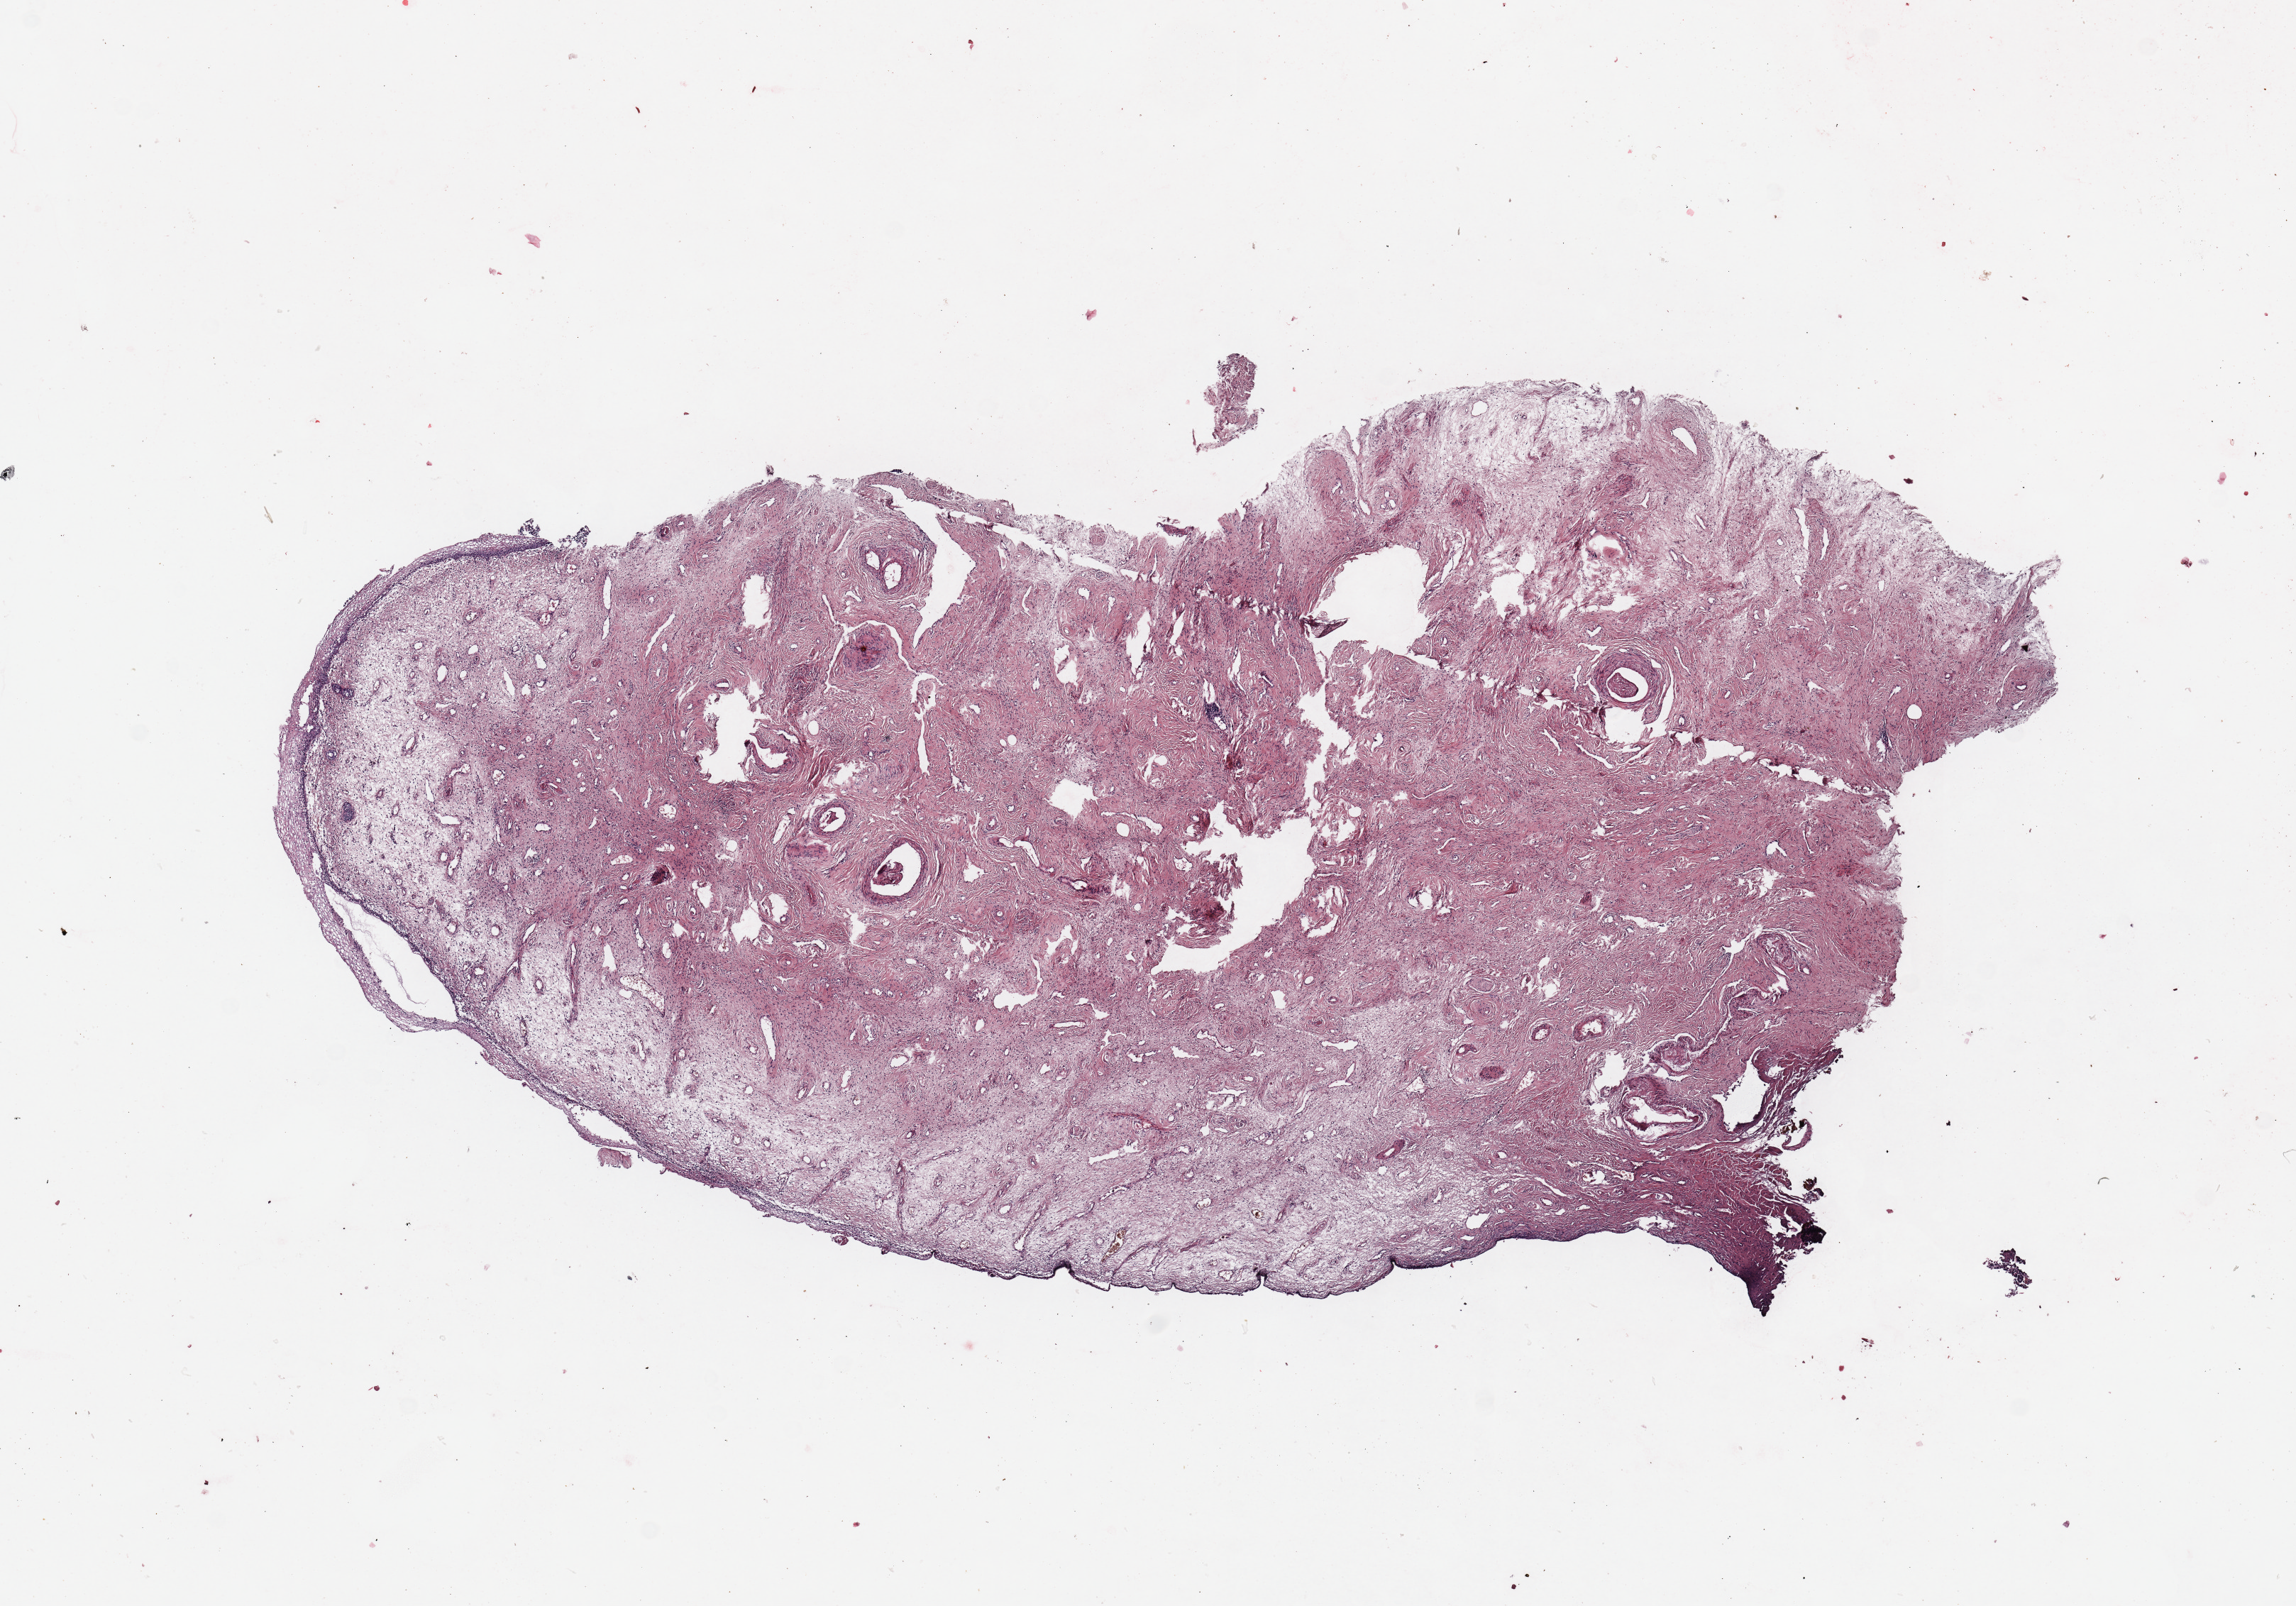
H&E whole-slide image, shown as a low-resolution overview of the whole scanned area (about 12.8 x 8.9 mm, acquisition: 20x scan); normal (non-tumour) tissue sample, uterus. 67-year-old female patient.
This section: normal (non-tumour) tissue from the same patient. Patient diagnosis: Endometrioid adenocarcinoma, NOS.